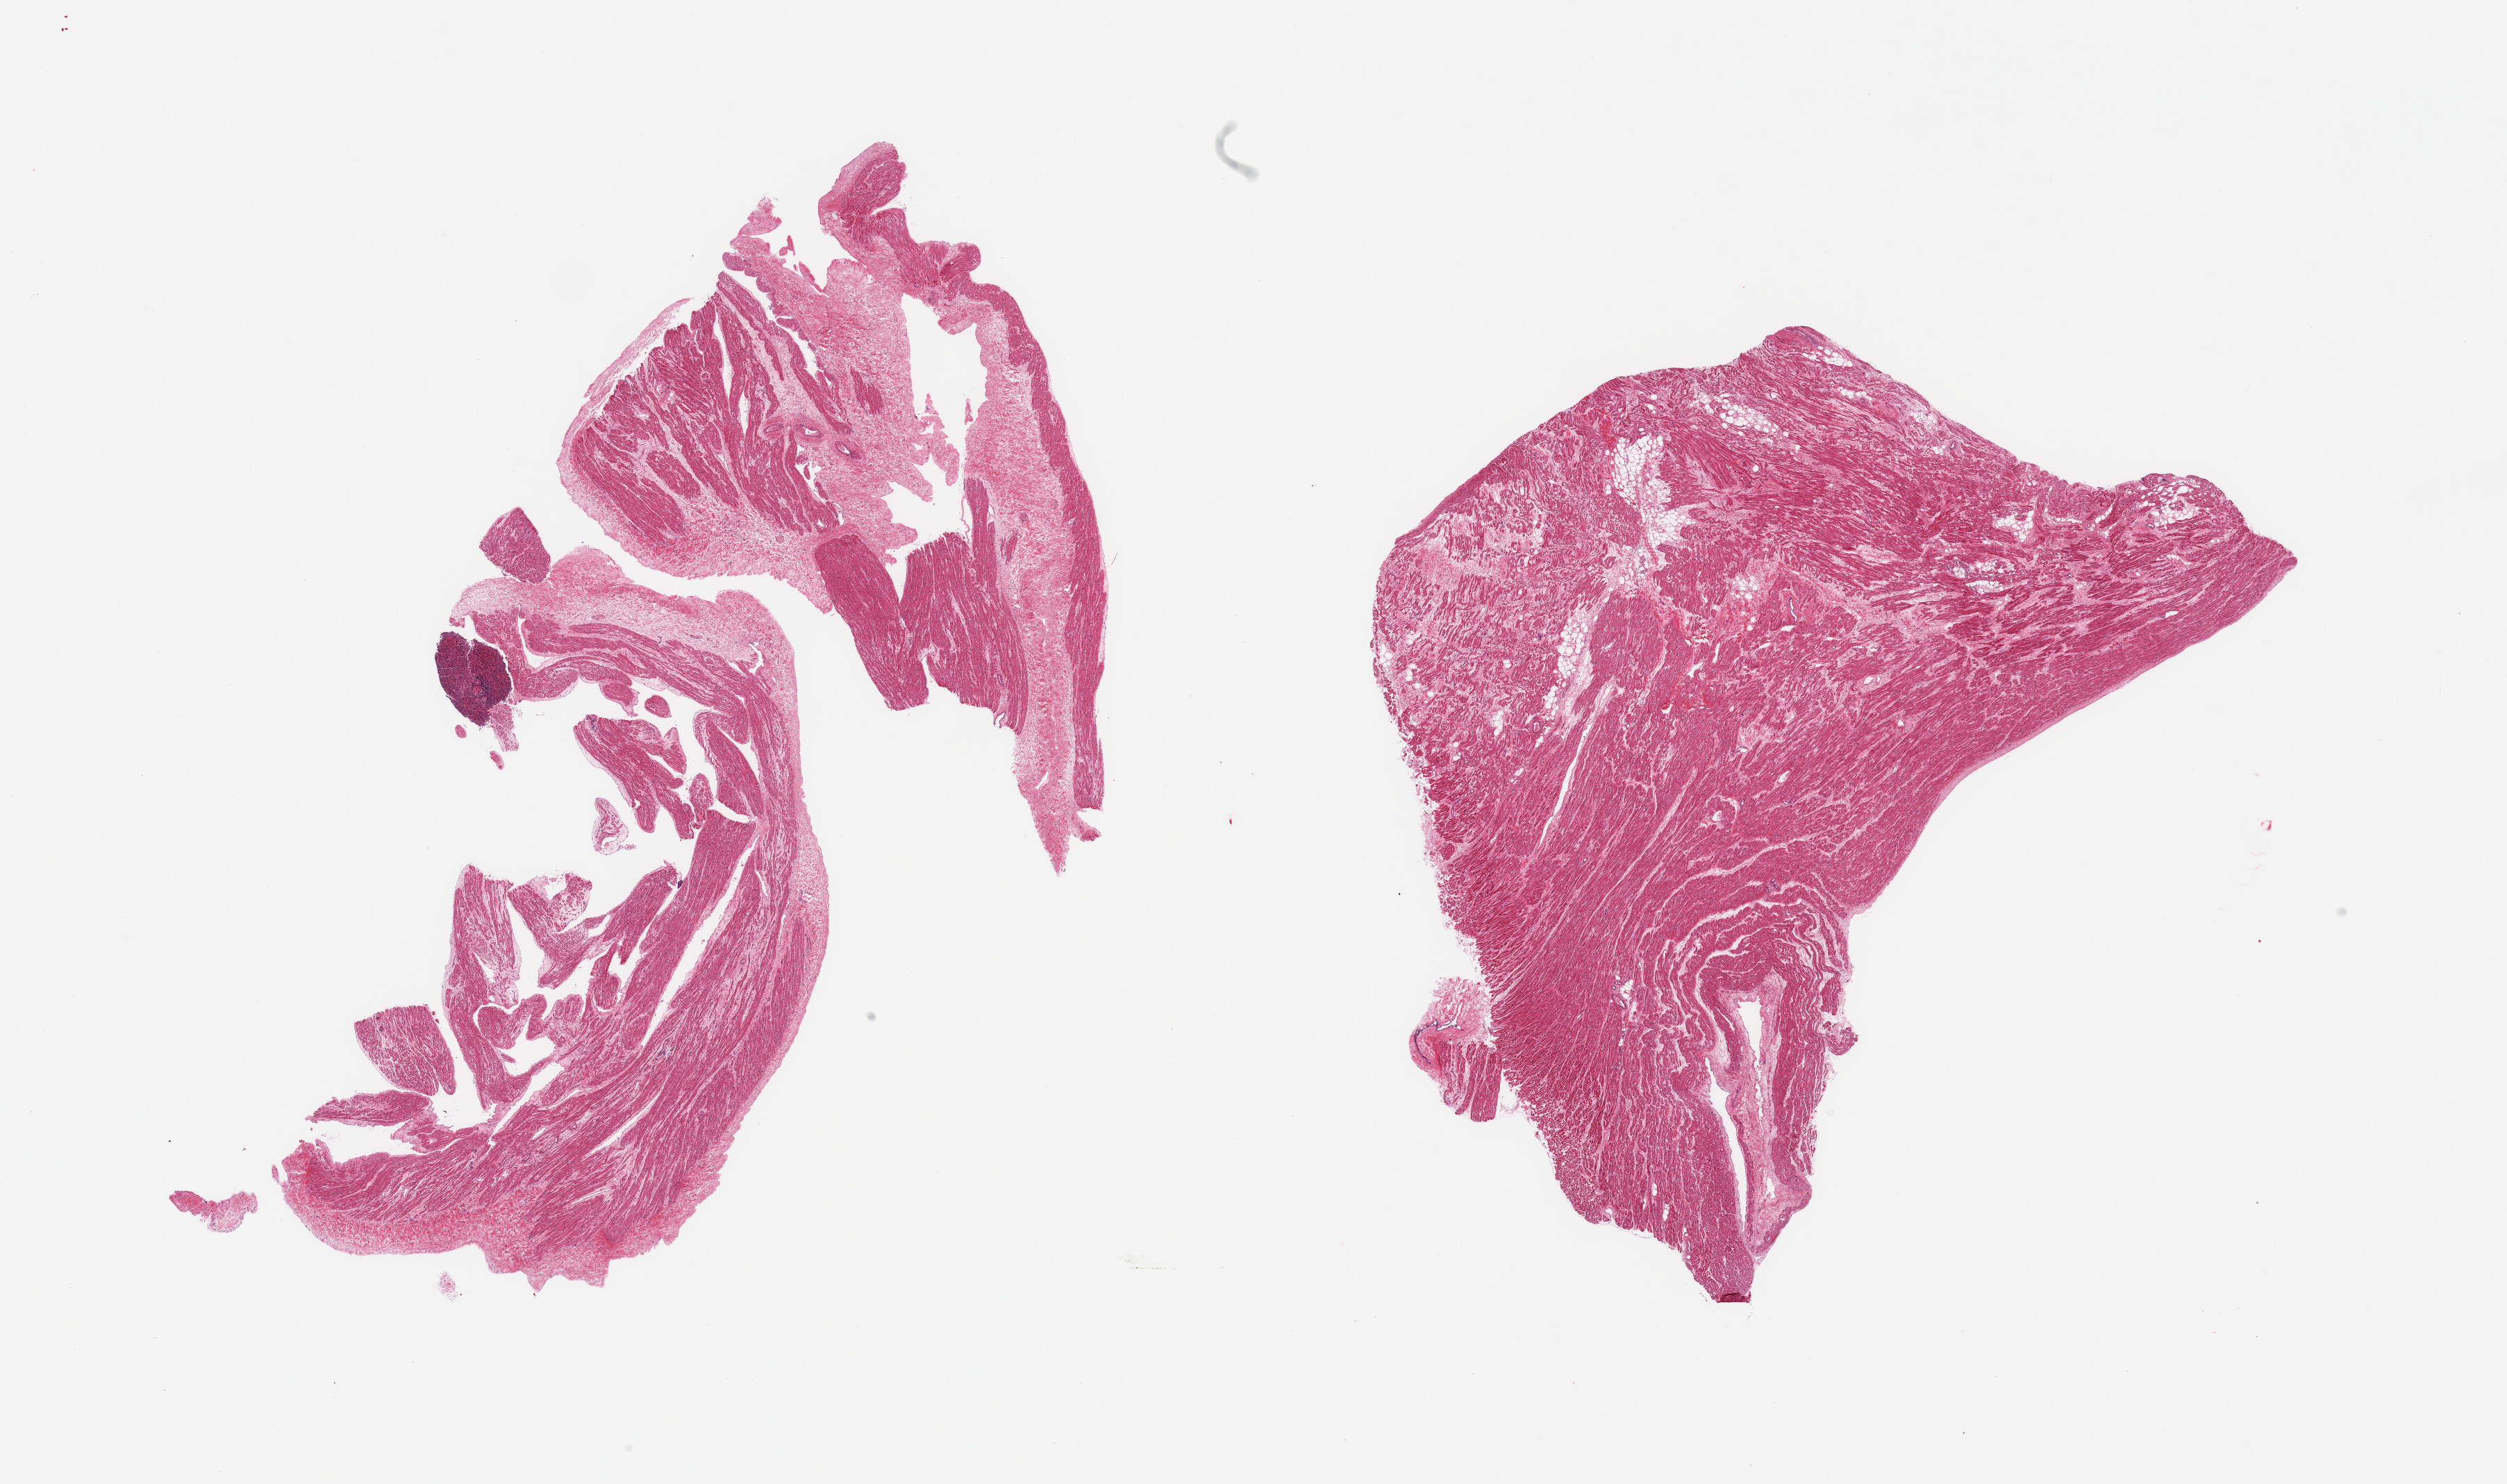
Digitized H&E-stained section — whole scanned area (about 28.5 x 16.9 mm) shown as a low-resolution overview, PAXgene-fixed paraffin-embedded (PFPE) section, section of auricular appendage (target tissue), tissue donor sample.
Review note (as recorded): 2 pieces; includes detached fragment of spleen, small amount of internal fat and fibrous component.